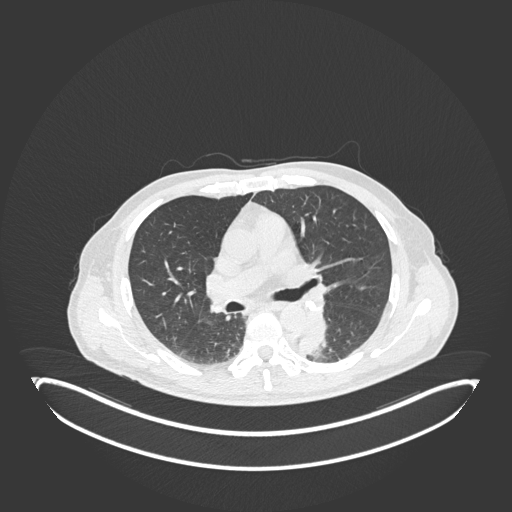
Chest CT, one axial slice; slice 121 of 251 in the series (ordered by position); 120 kVp; lung window (W 1500 / L -600 HU); 1 mm slice thickness; 512 × 512 image matrix, field of view 500 × 500 mm. Male patient, age 72 years. Case-level facts recorded for this patient, not image findings: clinical TNM (as recorded): T2b N0 M1.
Annotated regions visible in this slice (bounding box drawn by a radiologist):
- lung tumour (recorded histology: adenocarcinoma): bounding box [x1, y1, x2, y2] px = [298, 311, 333, 361]